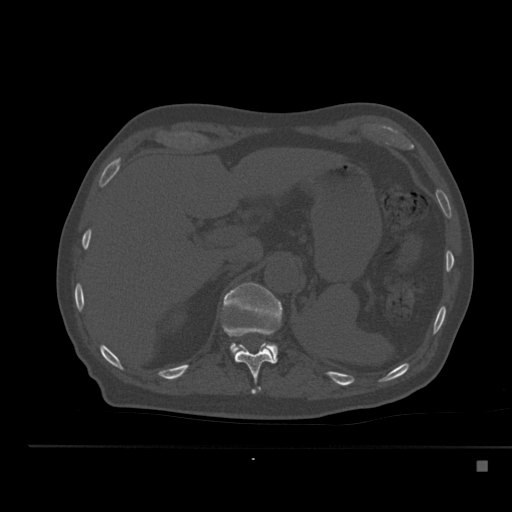
CT including the spine, one axial slice. Position 243 of 517 along the scan axis. Reconstruction kernel Br40s. Bone window (W 1800 / L 400 HU). 1.5 mm slice thickness. 512 × 512 image matrix, field of view 408 × 408 mm. Patient: male, 70 years. From the clinical record (not read from this slice): primary cancer: renal.
Annotated regions visible in this slice (semi-automatically segmented with operator editing):
- T11 vertebra: bounding box (x1, y1, x2, y2) in pixels: (222, 325, 273, 394)
- T12 vertebra: (223, 283, 282, 364)